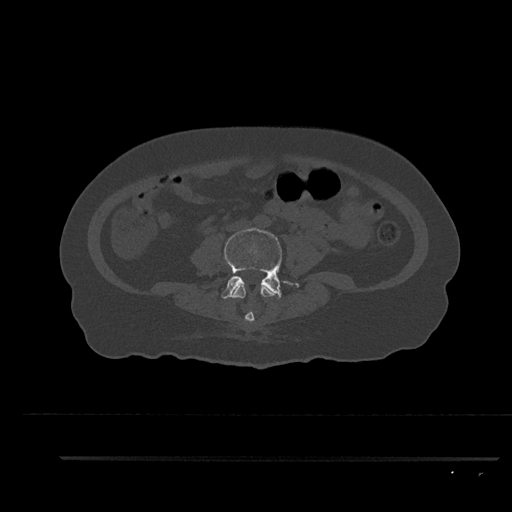
CT including the spine, one axial slice. Position 42 of 797 along the scan axis. Bone window (W 1800 / L 400 HU). 0.5 mm slice thickness. 512 × 512 image matrix, field of view 408 × 408 mm. Patient: female, 44 years. Case-level facts recorded for this patient, not image findings: primary cancer: renal.
Outlined on this slice (semi-automatically segmented with operator editing):
- L3 vertebra: box from (x=232, y=285) to (x=280, y=322) px
- L4 vertebra: (x=221, y=228)–(x=299, y=299)